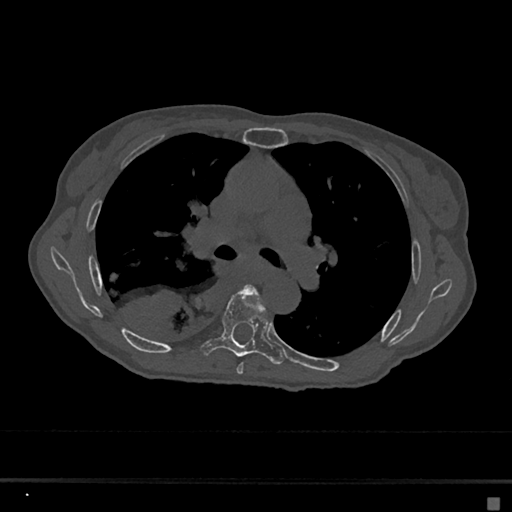
CT including the spine, one axial slice; position 427 of 797 along the scan axis; reconstruction kernel Br40s/3; 120 kVp; bone window (W 1800 / L 400 HU); 512 × 512 image matrix, field of view 360 × 360 mm. Female patient, age 68 years. Case-level facts recorded for this patient, not image findings: primary cancer: renal.
Annotated regions visible in this slice (semi-automatic segmentation, software-assisted and operator-edited):
- T5 vertebra: bounding box <236,285,260,375> (left, top, right, bottom; pixels)
- T6 vertebra: <201,288,284,365>